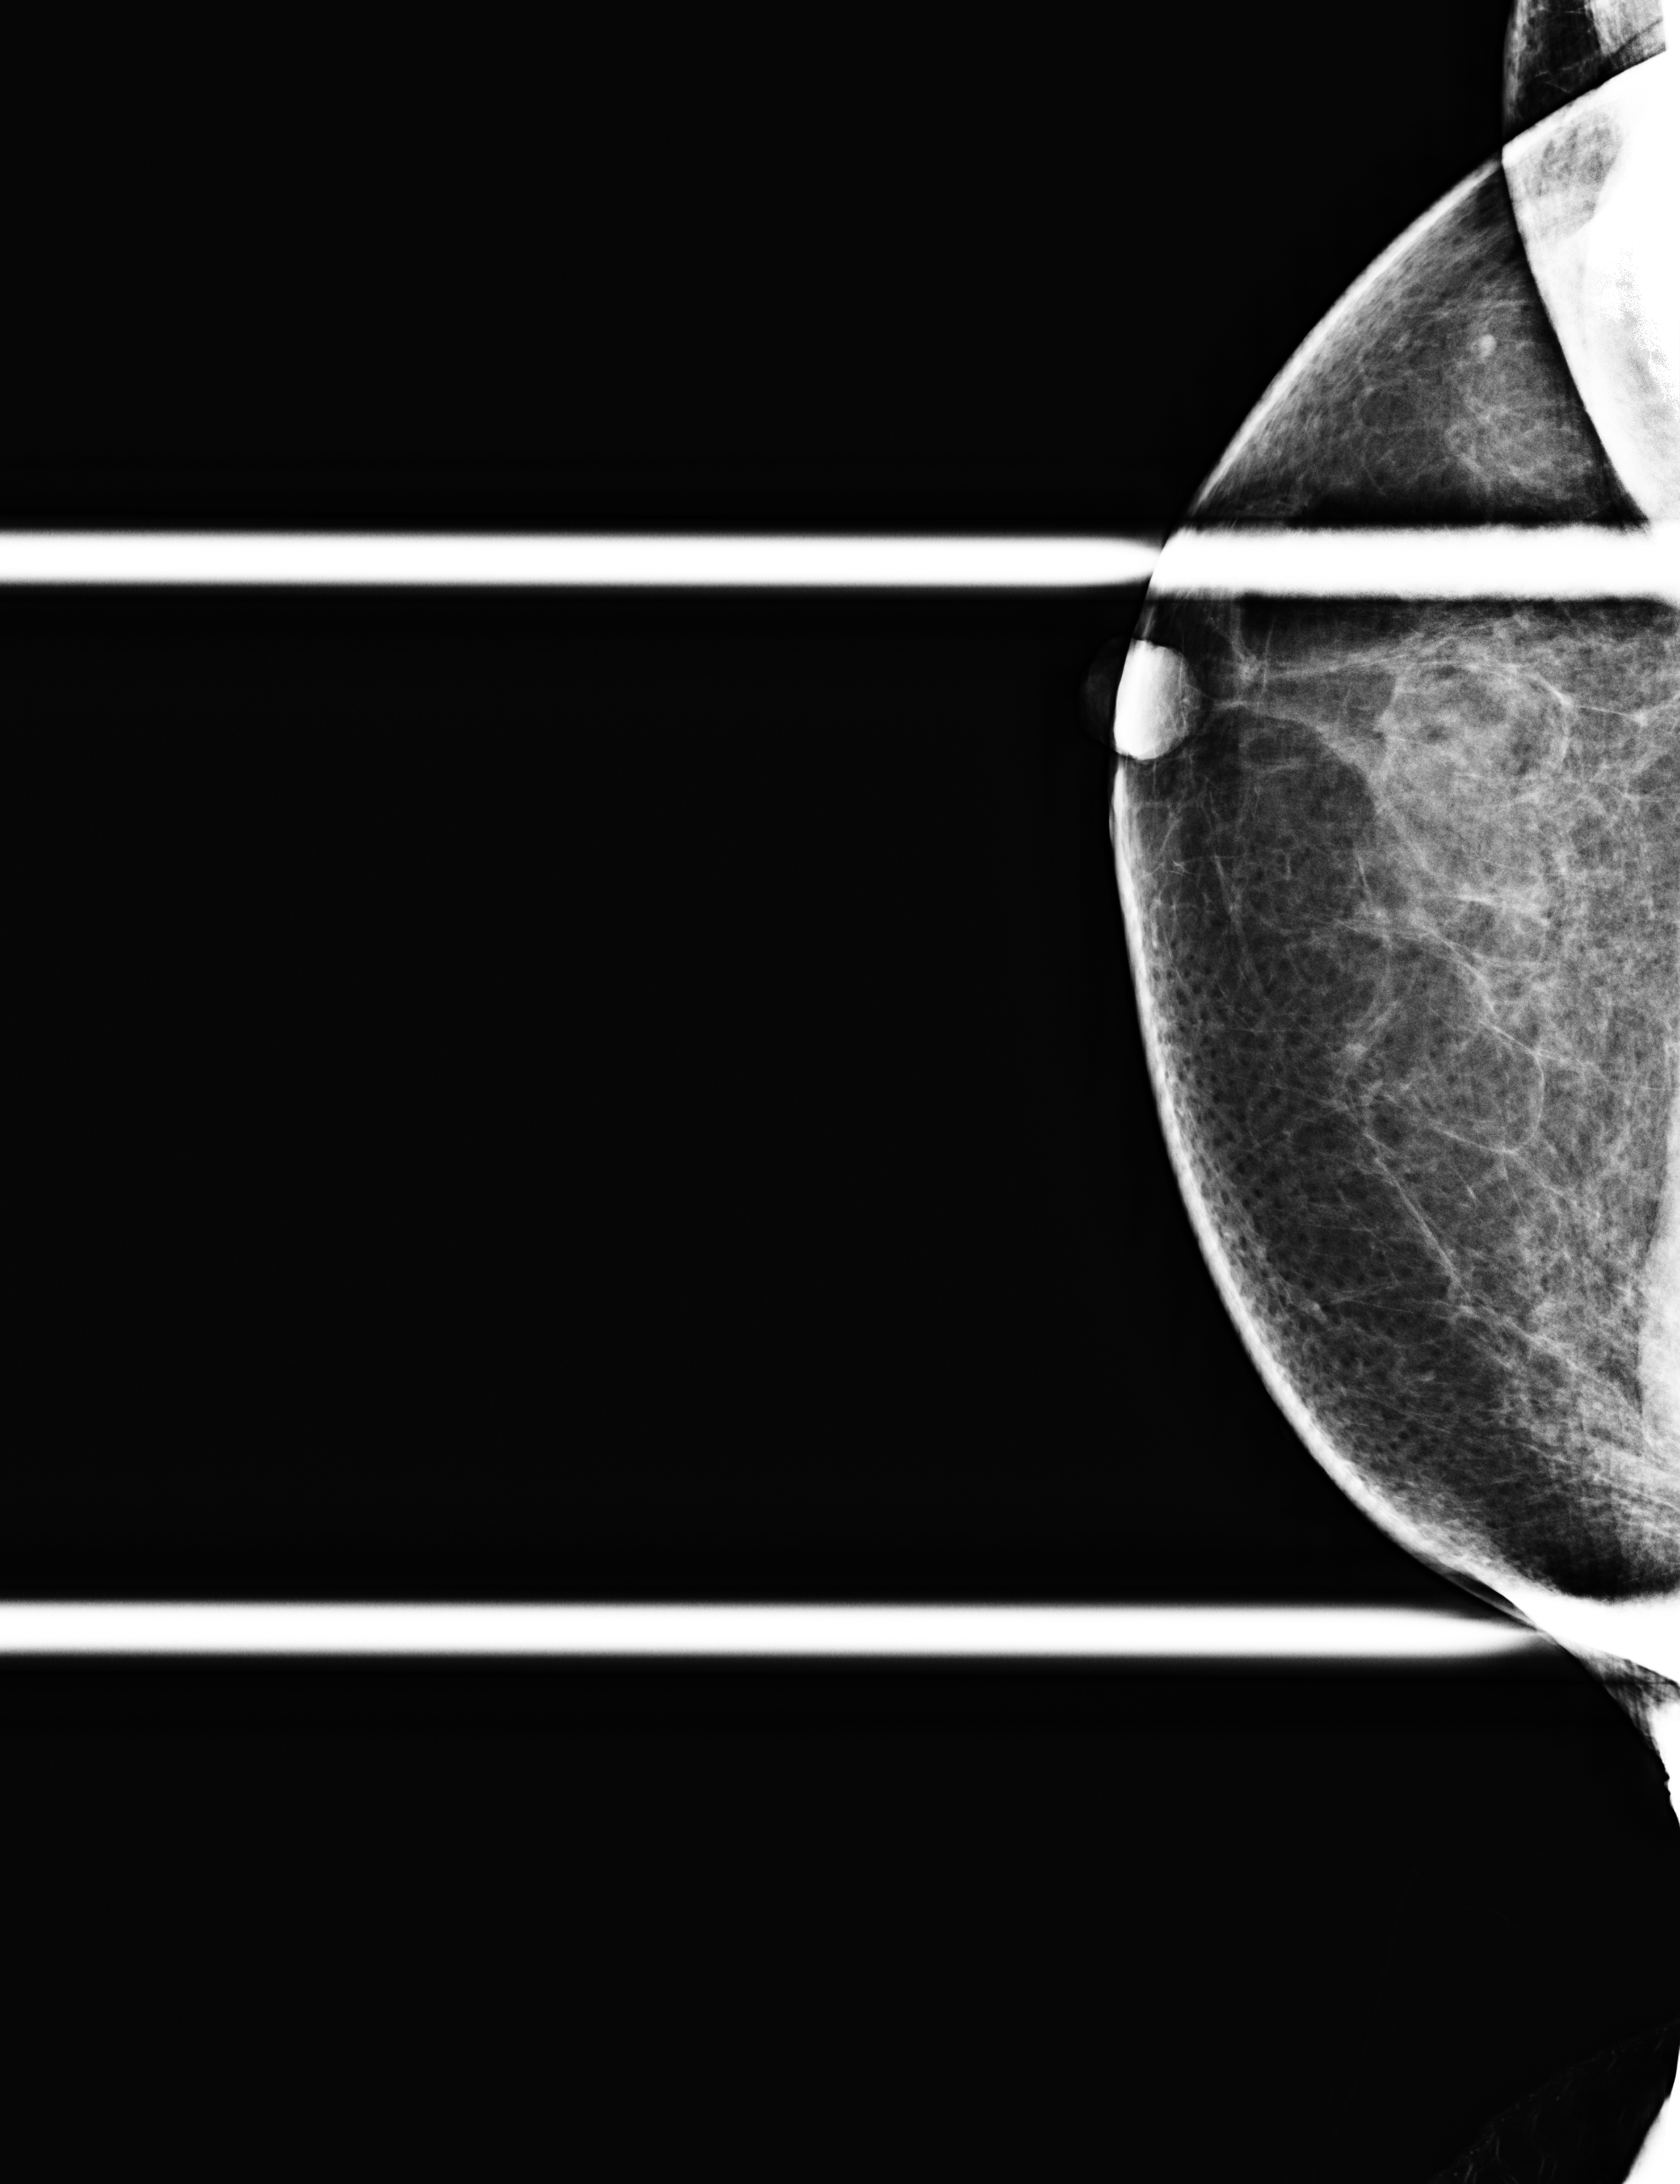
Digital mammogram (FFDM), right breast, CC view (spot compression), additional (diagnostic) view, compressed breast thickness 57 mm. Female patient, age 61 years.
Final BI-RADS assessment for this screening round (tomosynthesis exam, both breasts): category 2.